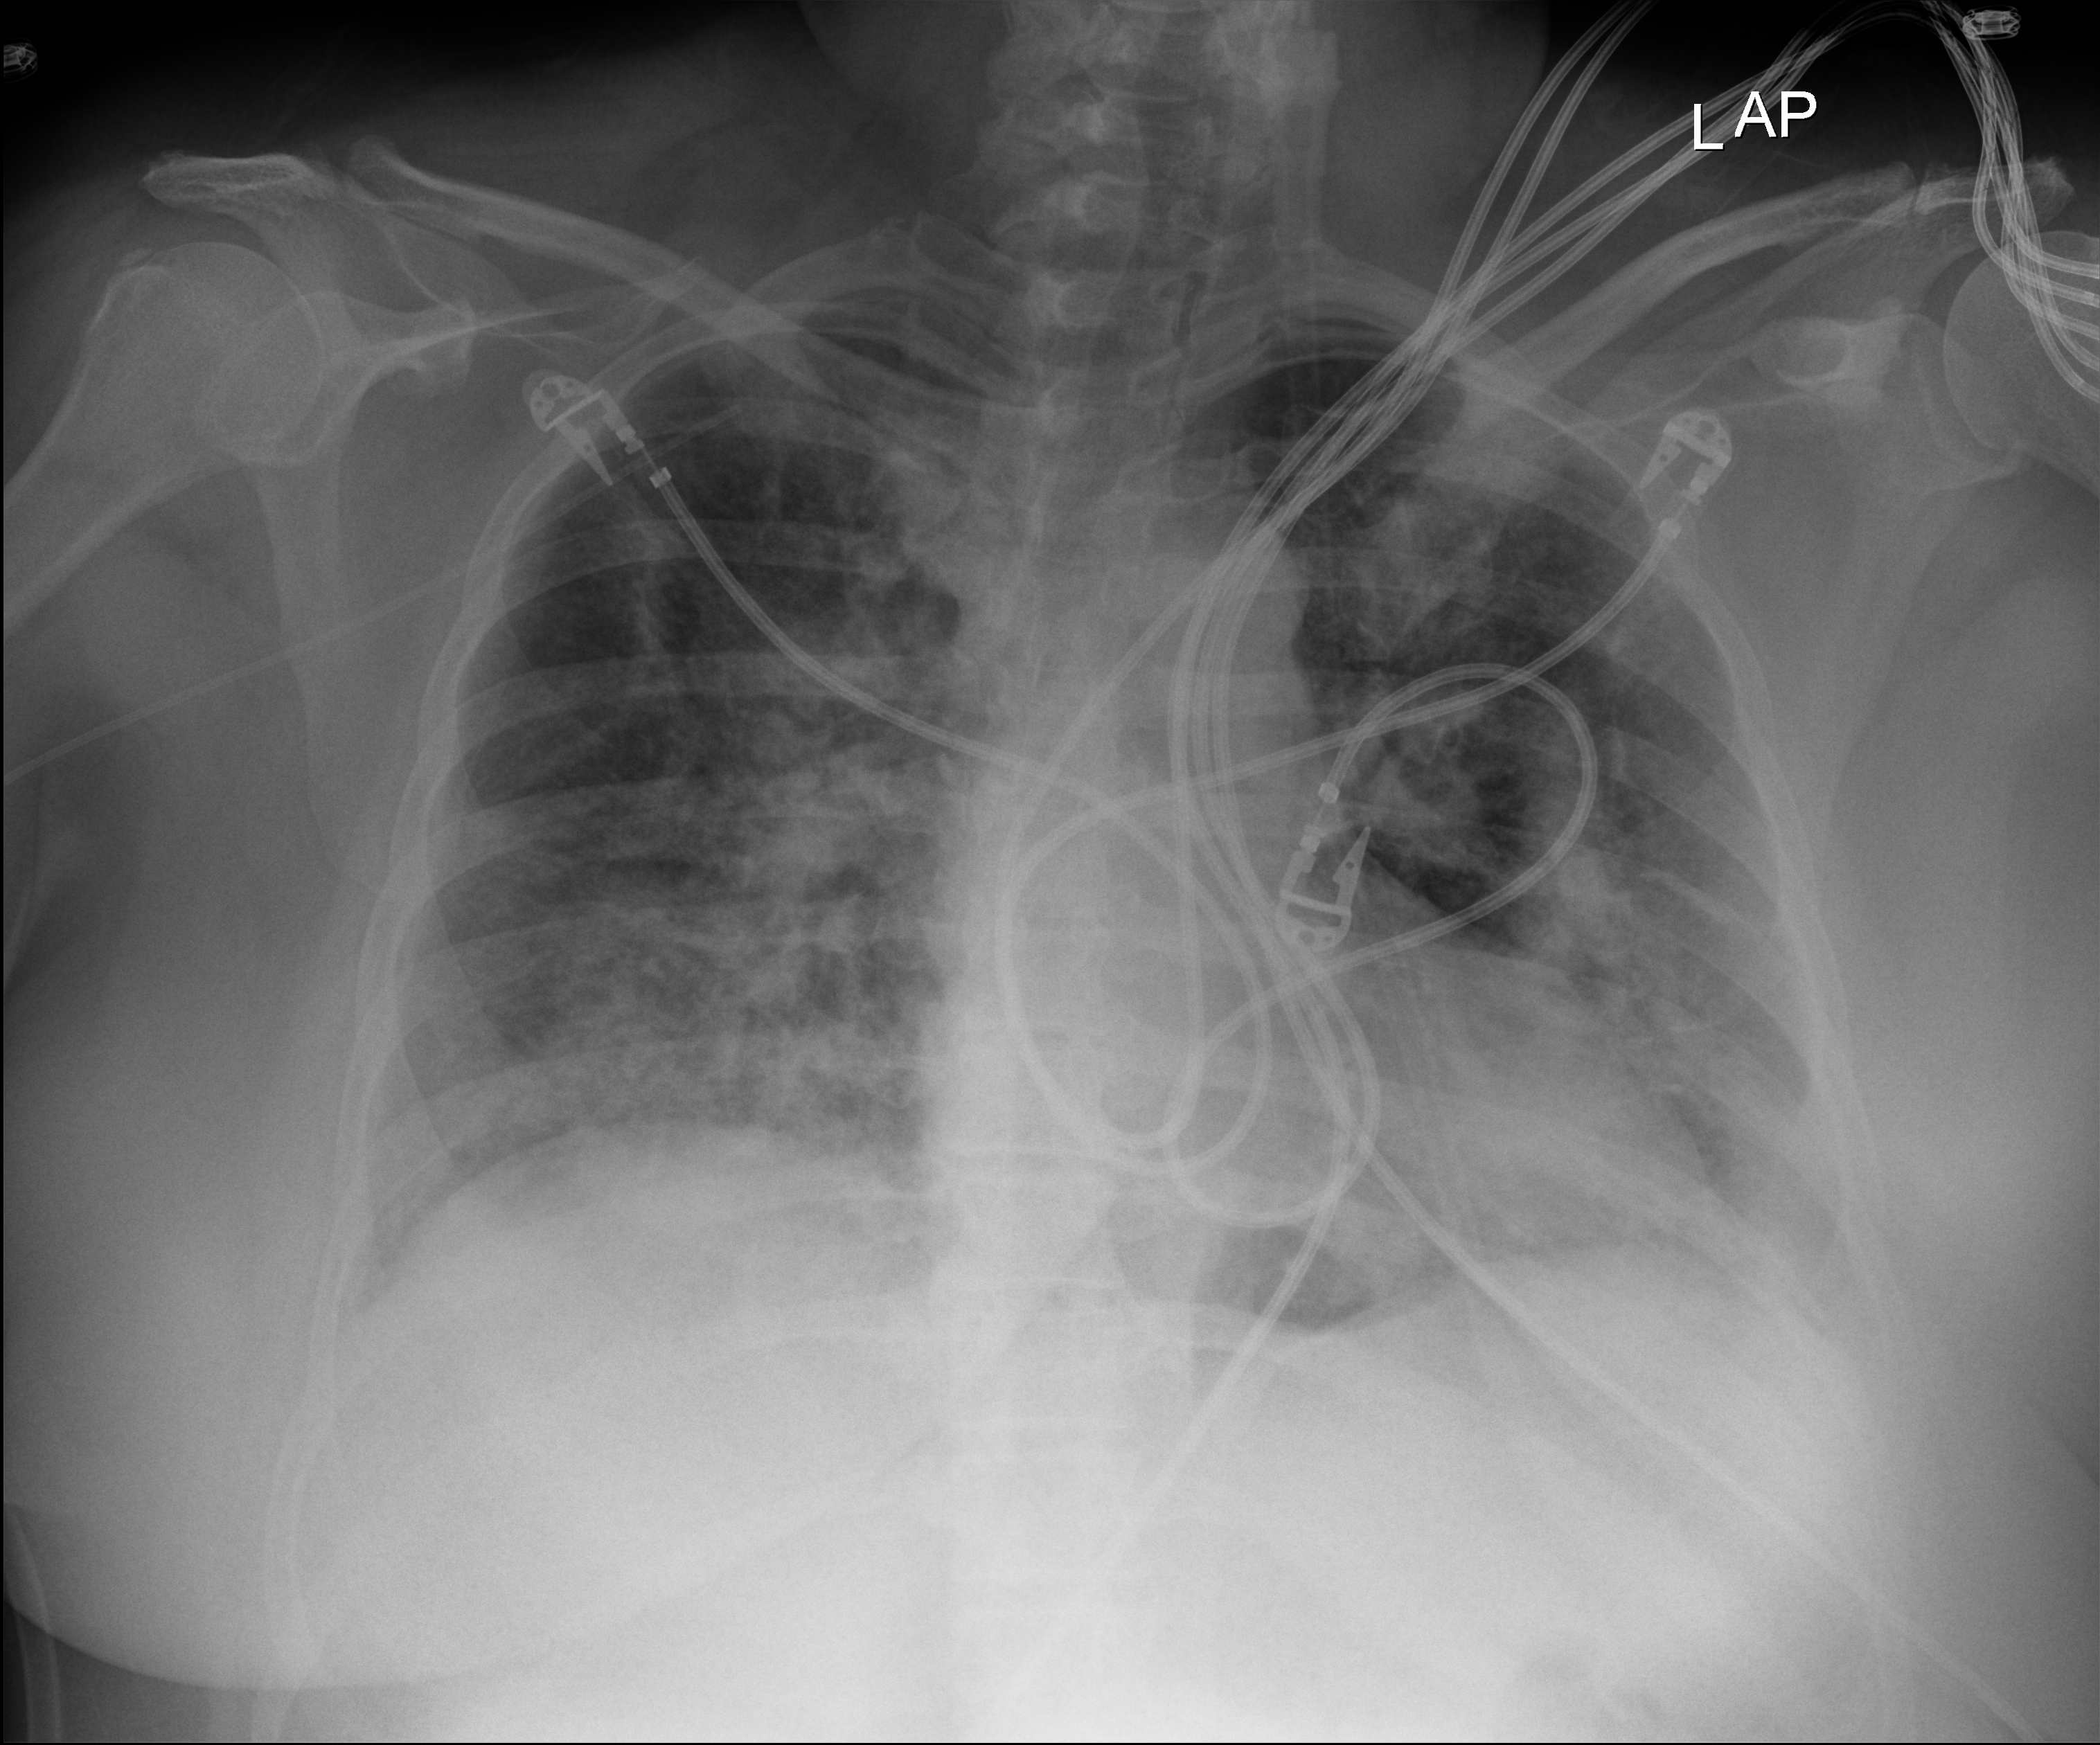
Chest X-ray (portable). Patient hospitalised with COVID-19; female, aged 18–59 years.
Hospital-stay facts (about this admission, not read from this image; timing relative to this image not recorded): hypertension (admission record): yes; admitted to intensive care during this hospital stay: no; other chronic lung disease (admission record): no.